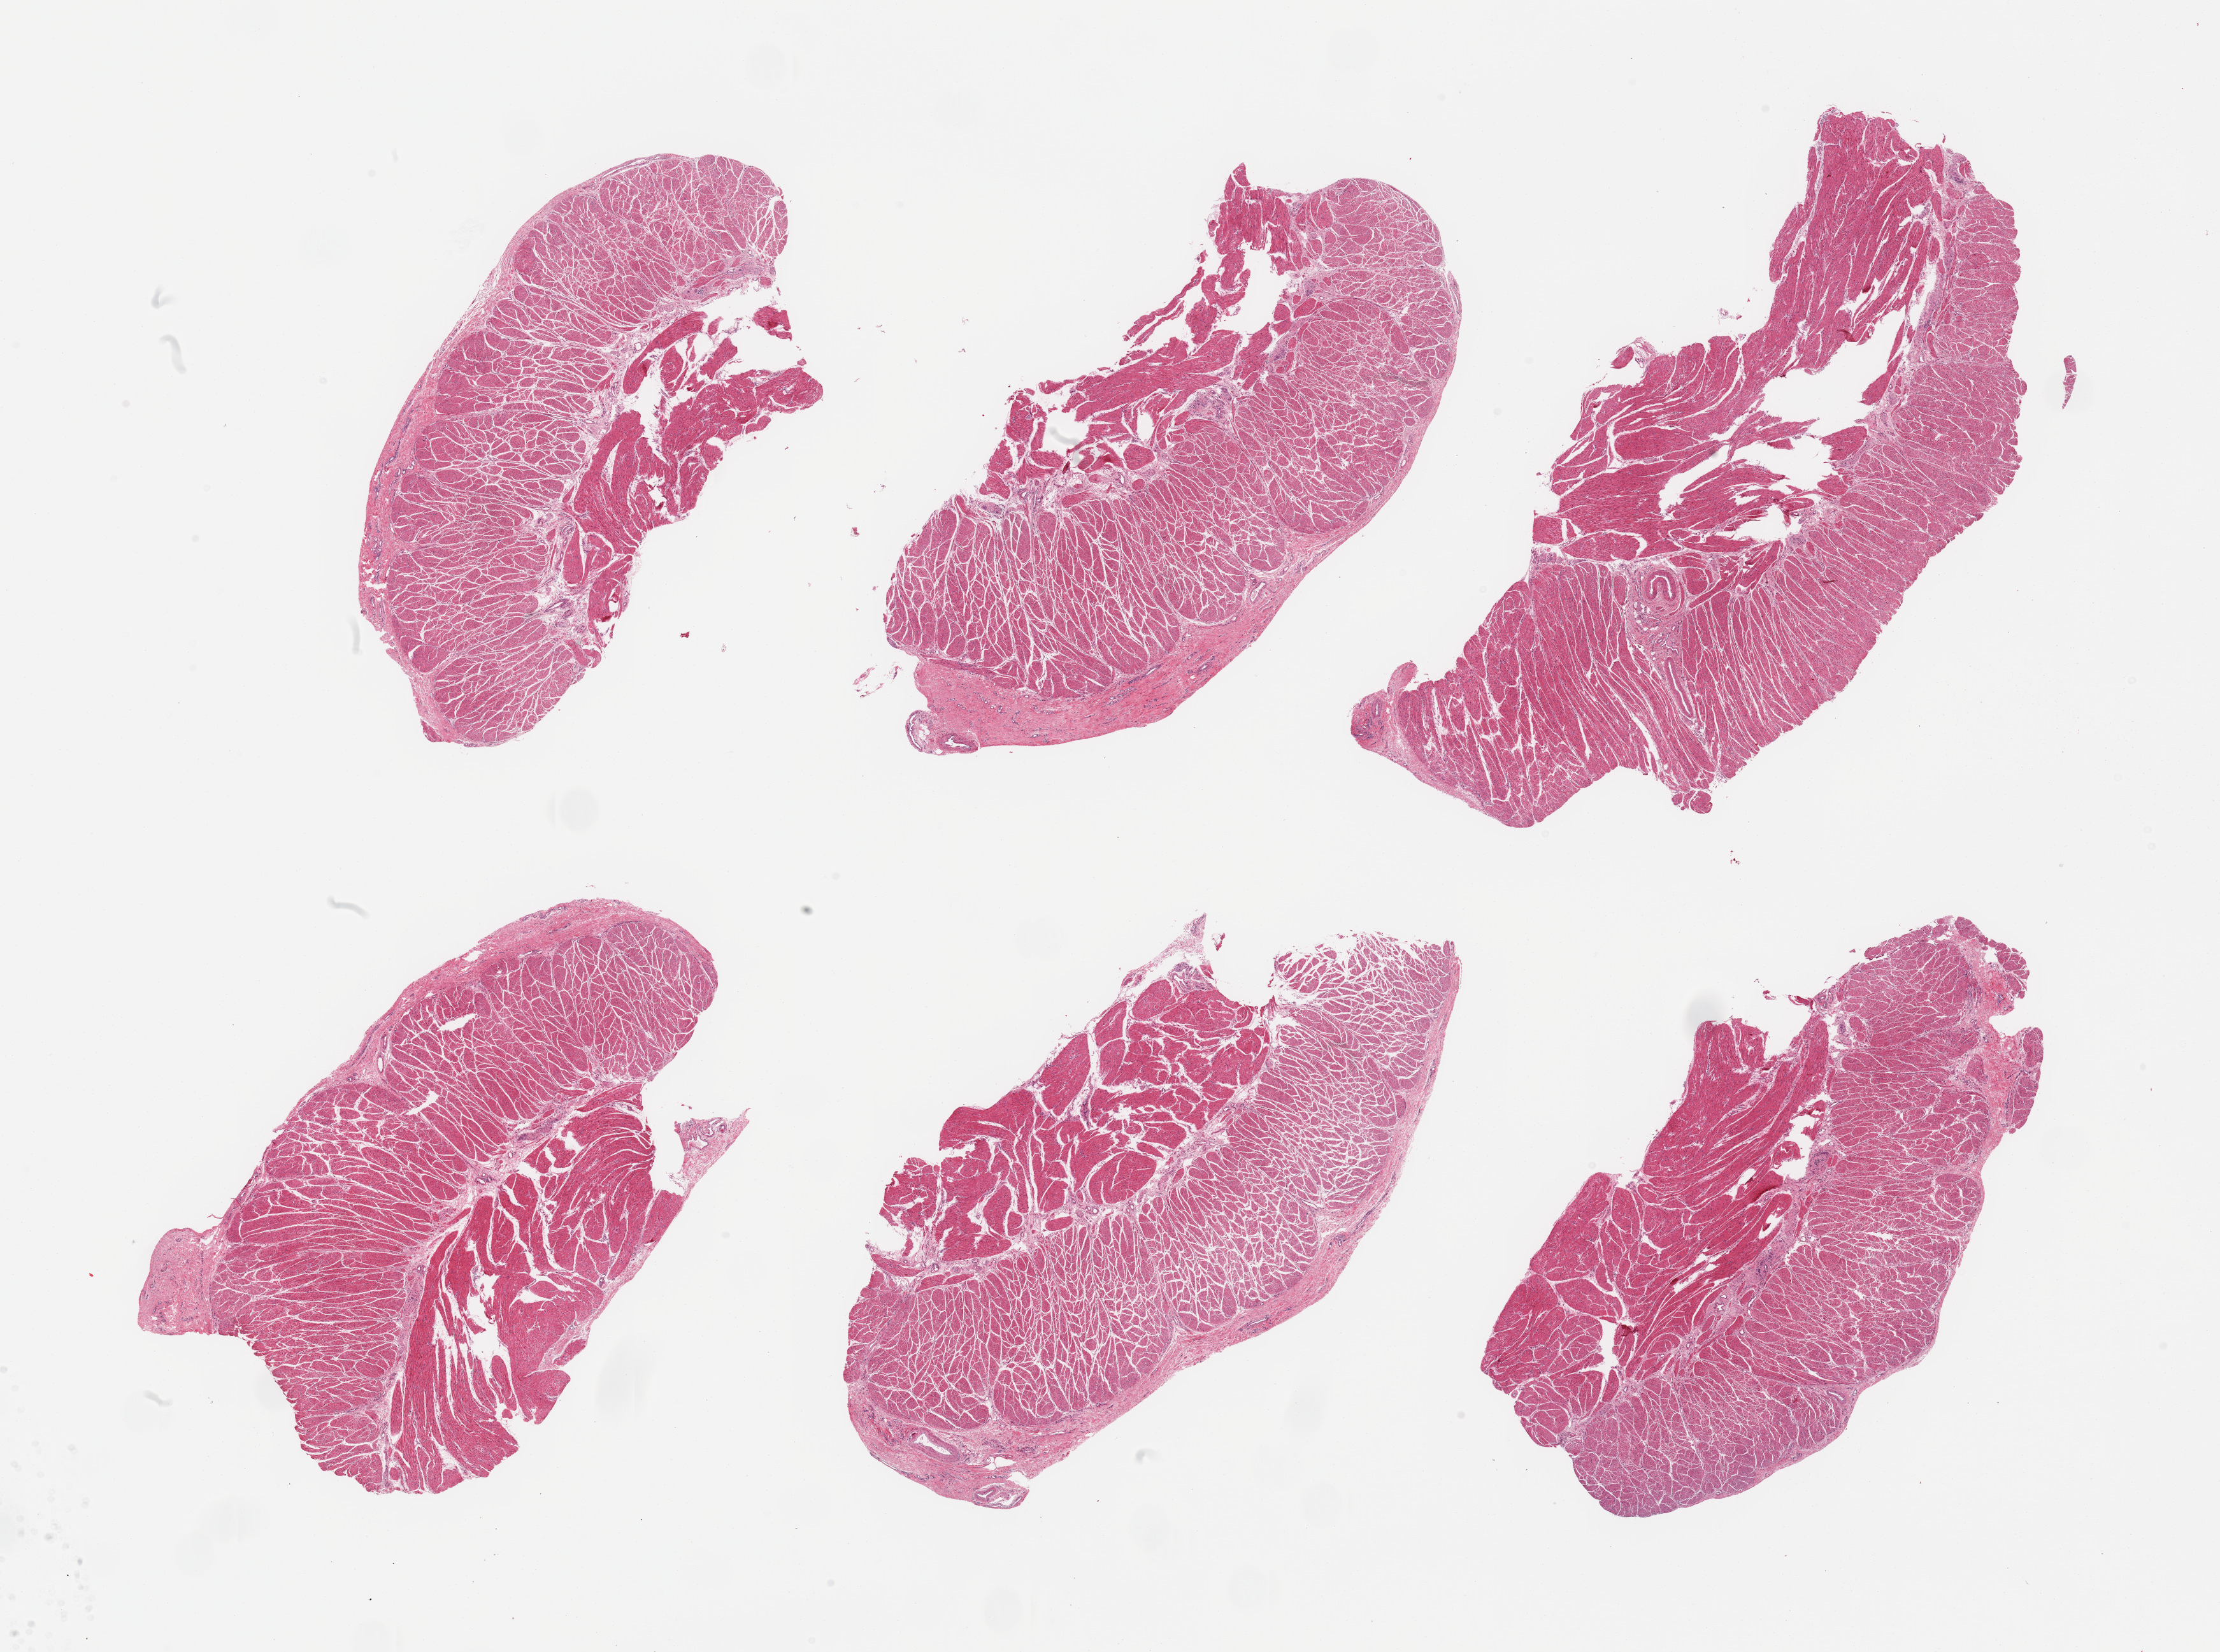
Digitized haematoxylin and eosin-stained section, shown as a low-resolution overview of the whole scanned area (about 27.6 x 20.5 mm, acquisition: 20x scan). PAXgene-fixed, paraffin-embedded tissue. Sampled site (target tissue): esophageal muscle. Tissue donor sample. Donor: male.
* pathologist's review note for this sample: 6 pieces; well dissected